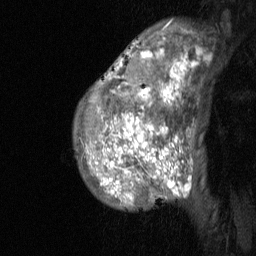
Breast MRI (dynamic contrast-enhanced), one sagittal slice; slice 46 of 64 in the series (ordered by position); dynamic contrast-enhanced study with each time point stored as its own series, time point 2 of 3 at this slice position (early post-contrast, ordered by acquisition time); 1.5 T; TE 4.8 ms, TR 27 ms; 2 mm slice thickness; 256 × 256 image matrix. Patient: female, 36 years. Case-level facts recorded for this patient, not image findings: setting: breast cancer imaged before/during neoadjuvant chemotherapy; receptor status: HR-positive, HER2-negative.
Structures marked on this image (semi-automatic segmentation, software-assisted and operator-edited):
- analysis volume of interest (the breast-tissue region the enhancement analysis was run in; not a lesion): bounding box [x1, y1, x2, y2] px = [73, 20, 201, 211]
- tumour enhancement mask (voxels above the 90 % enhancement threshold inside the analysis volume of interest): [101, 49, 190, 194]